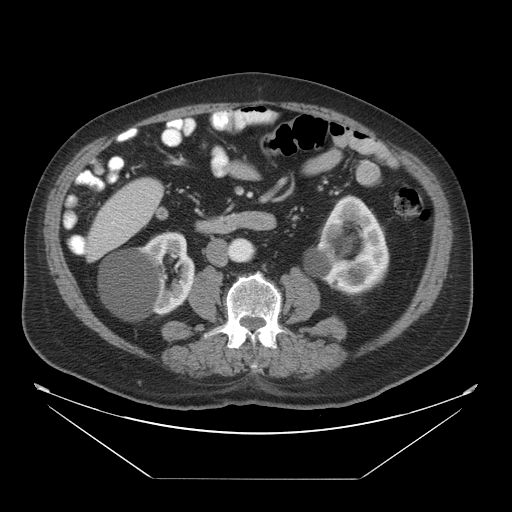
Contrast-enhanced abdominal CT, one axial slice. Reconstruction kernel STANDARD. 120 kVp. Intravenous contrast given. Soft-tissue window (W 400 / L 40 HU). 5 mm slice thickness. 512 × 512 image matrix. Male patient, age 87 years. From the clinical record (not read from this slice): diagnosis: colorectal cancer liver metastases, imaged before liver resection; multiple liver metastases: no; largest metastasis: 4.5 cm; chemotherapy before resection: no.
Outlined on this slice (expert manual segmentation):
- liver: box from (x=85, y=178) to (x=164, y=261) px